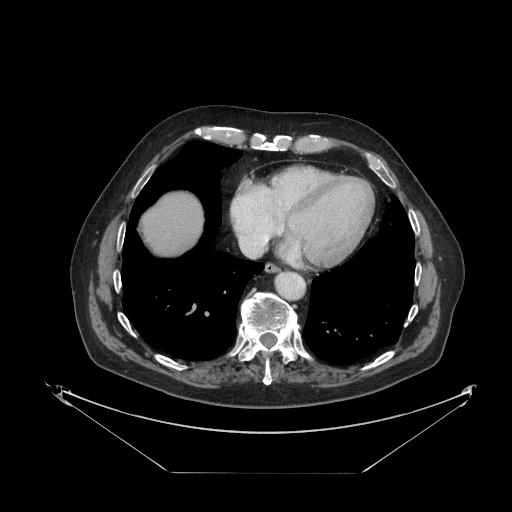
Contrast-enhanced abdominal CT, one axial slice. Slice 119 of 121 in the series (ordered by position). 120 kVp. Intravenous contrast given. Soft-tissue window (W 400 / L 40 HU). 2.5 mm slice thickness. 512 × 512 image matrix, field of view 500 × 500 mm. Male patient, age 68 years. From the clinical record (not read from this slice): diagnosis: colorectal cancer liver metastases, imaged before liver resection.
Outlined on this slice (expert manual segmentation):
- liver: bounding box (x1, y1, x2, y2) in pixels: (142, 193, 203, 254)
- planned liver remnant (the part of the liver to remain after resection): (142, 193, 203, 255)